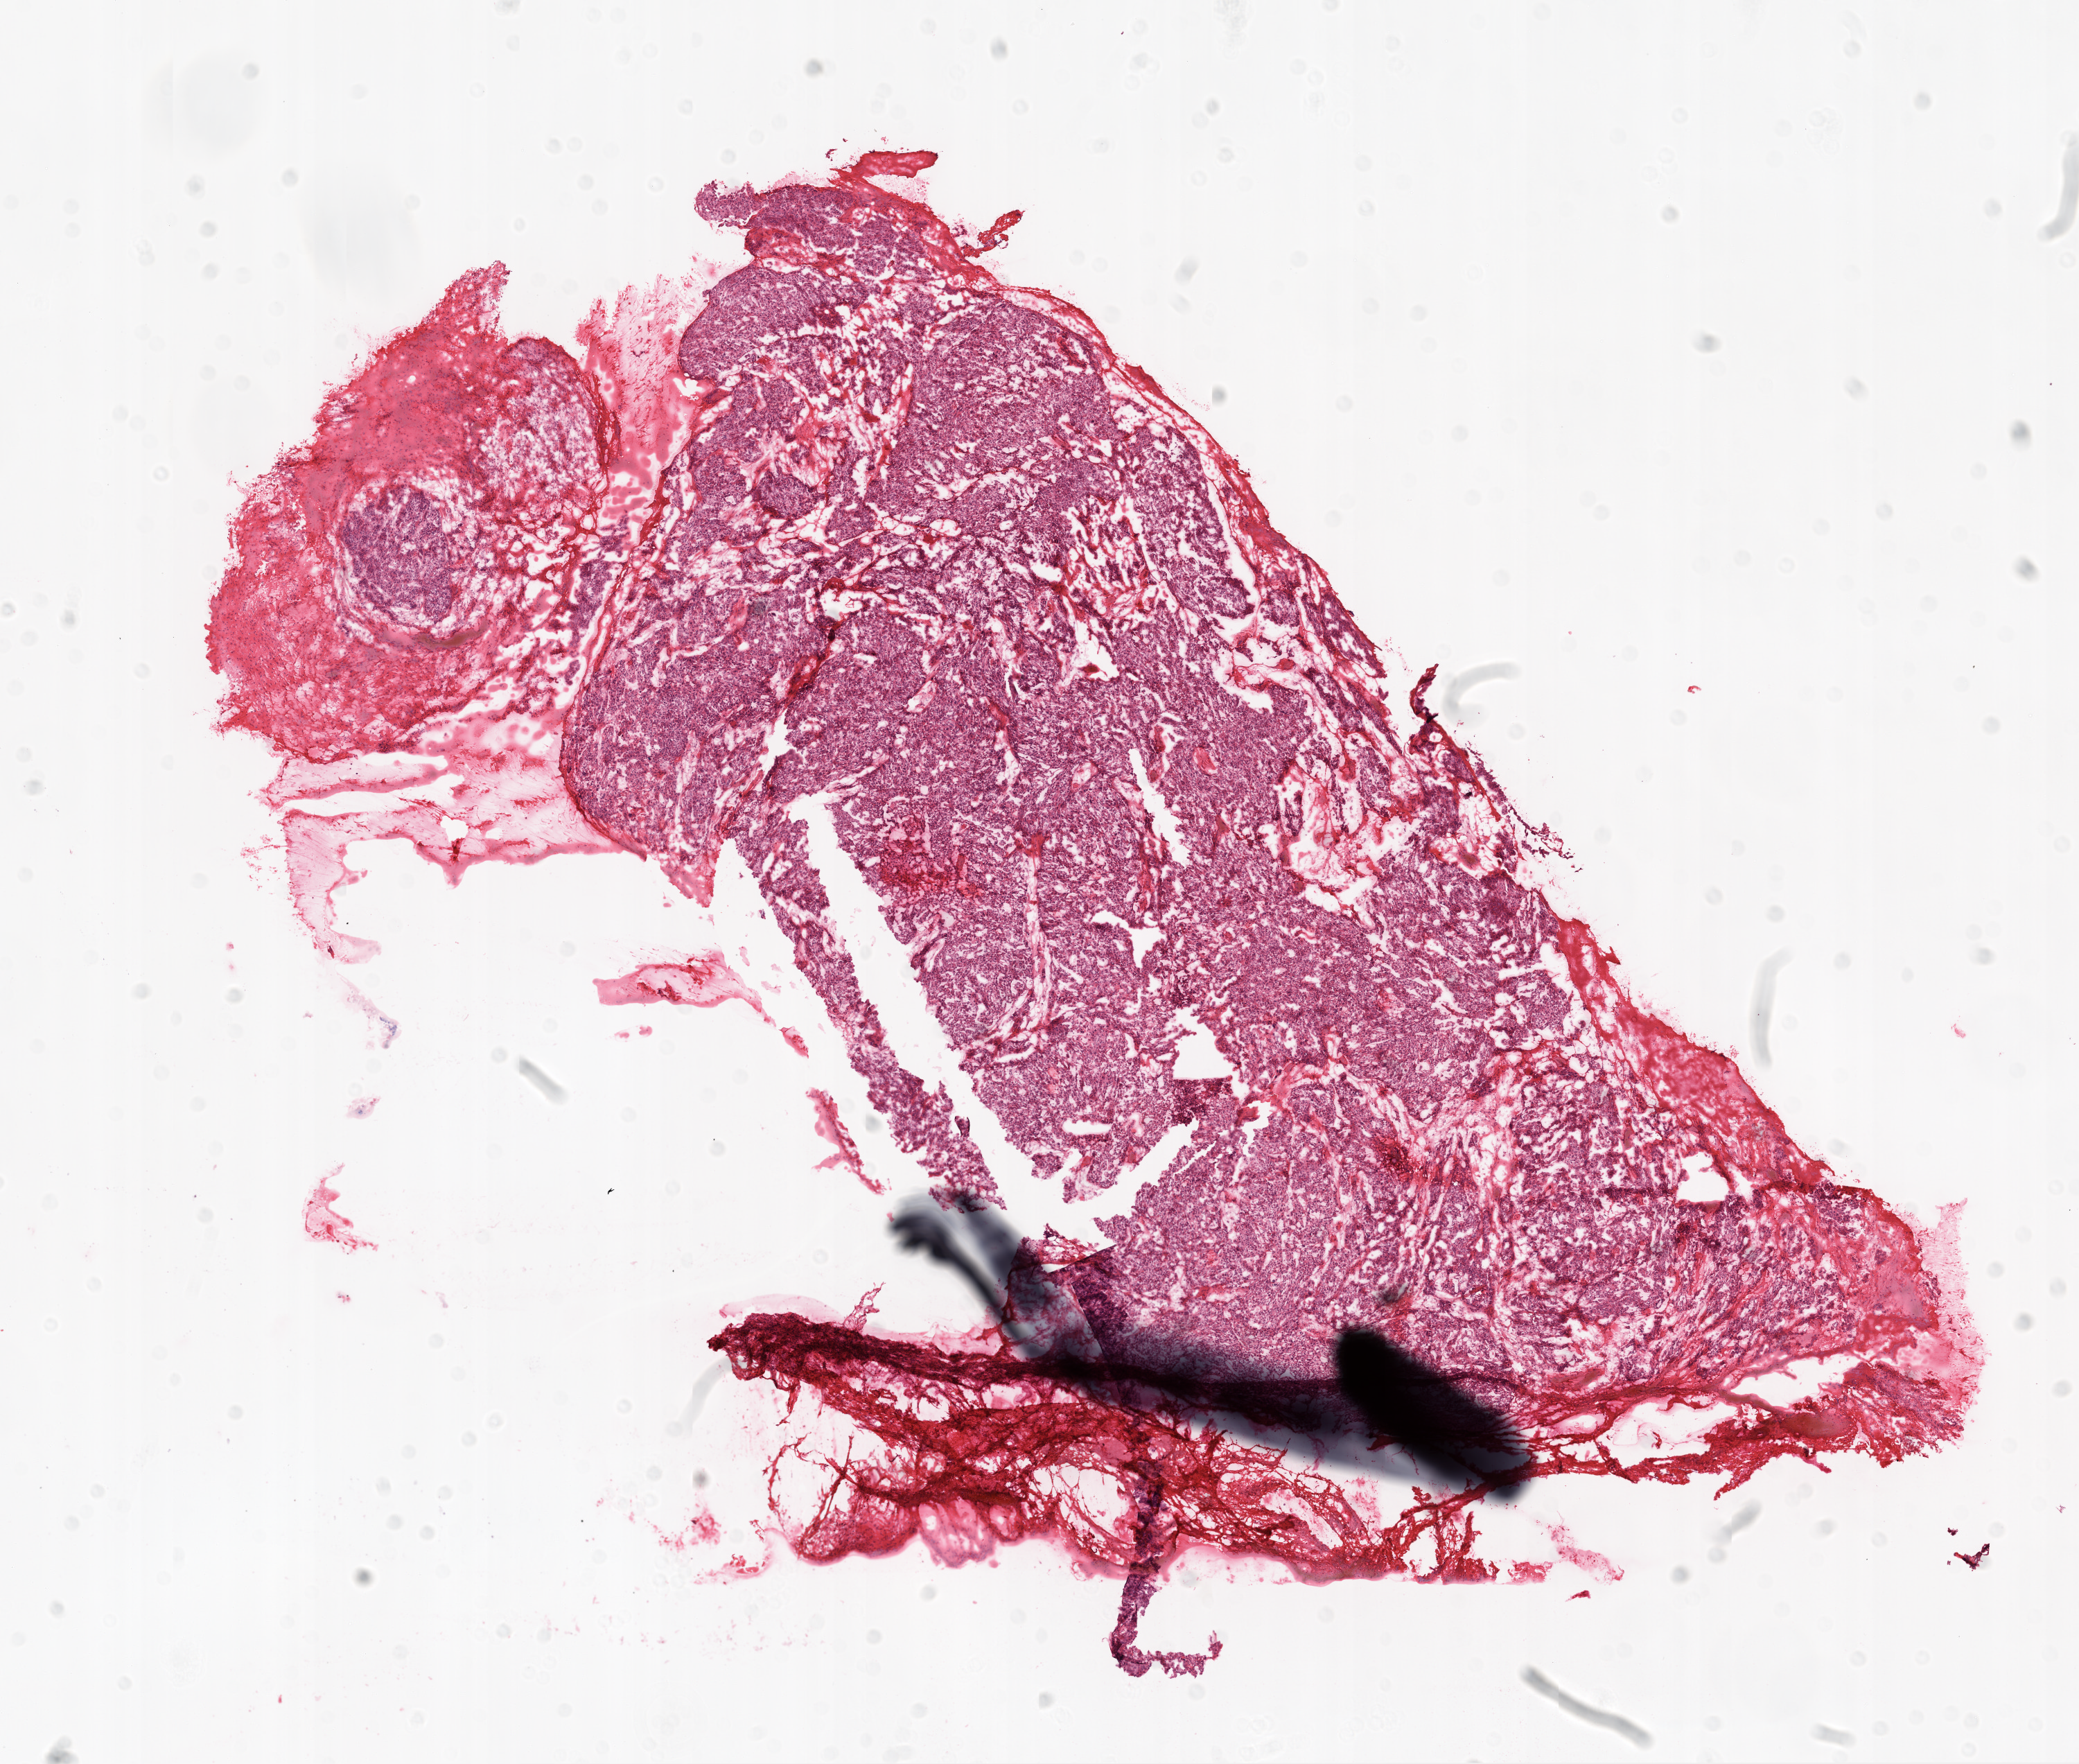
Hematoxylin and eosin (H&E) stained whole-slide image, shown as a low-resolution overview of the whole scanned area (about 12.0 x 10.2 mm). Frozen section from the top of the tissue portion. Primary tumour sample from the ovary. Female patient; age at initial diagnosis 55 years. Histologic grade: G3 (poorly differentiated). Composition of this section per pathologist review: tumour cells 95%, tumour nuclei 95%, normal cells 0%, stromal cells 5%, necrosis 0%.
Pathologic diagnosis: Serous cystadenocarcinoma, NOS. FIGO stage: IIIC.